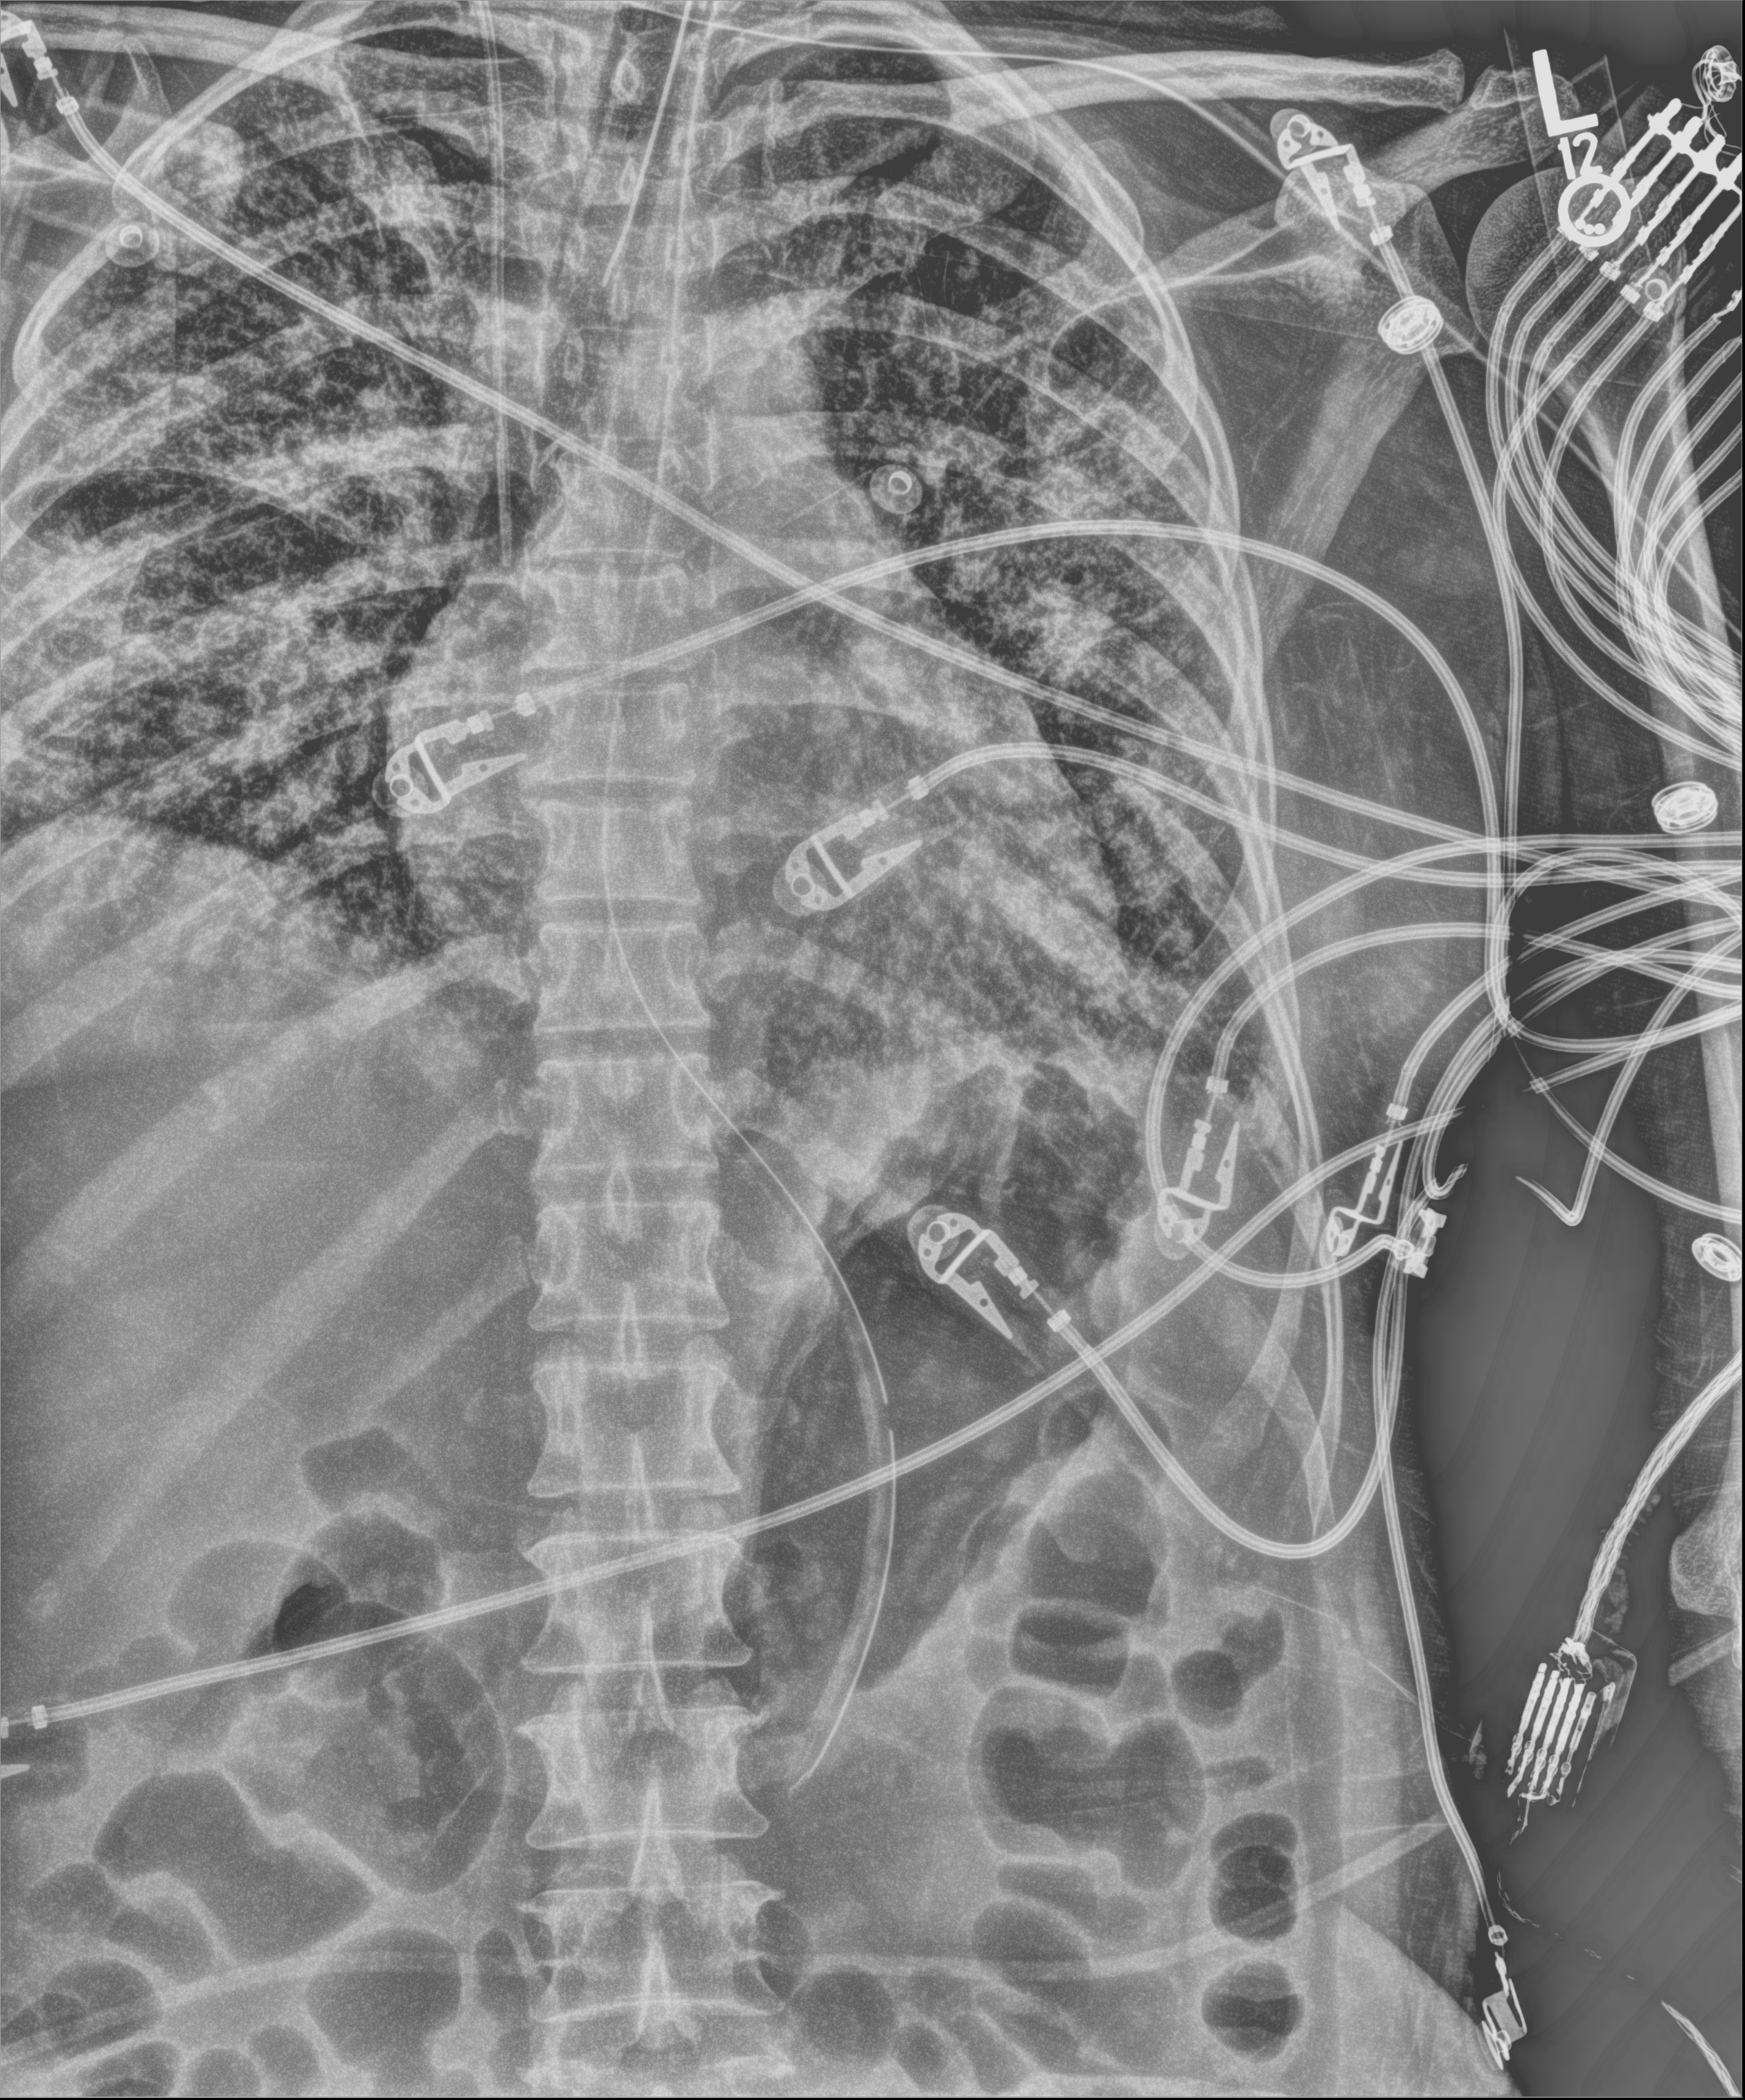
Bedside chest radiograph (digital radiography), anteroposterior (AP) projection. Patient hospitalised with COVID-19; female, aged 18–59 years.
Hospital-stay facts (about this admission, not read from this image; timing relative to this image not recorded):
- mechanically ventilated during this hospital stay: yes